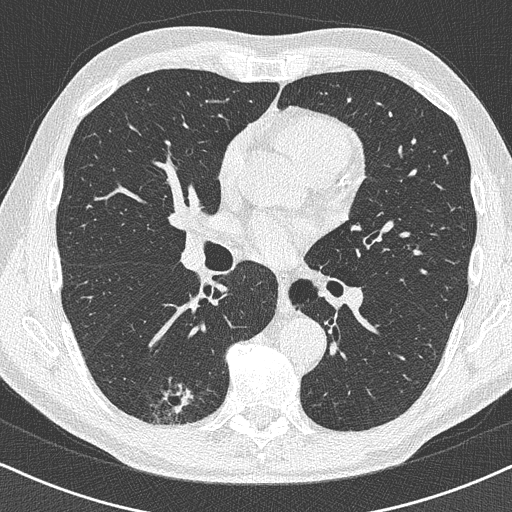
Low-dose screening chest CT, axial slice. Baseline annual screen. Lung window (W 1500 / L -600 HU). Lung (sharp) reconstruction kernel (B50f). Male, age 63 years at enrolment.
Lesion marked by an expert reader, bounding box <138,374,209,431> (left, top, right, bottom; pixels). The exam's reader record, not a measurement of the box and not confirmed to be the same lesion: non-calcified nodule or mass ≥4 mm, right lower lobe, 16 × 13 mm, poorly defined margins. Participant outcome: lung cancer diagnosed 74 days after this screen — adenocarcinoma, NOS, right lower lobe, moderately differentiated (G2), stage IA (AJCC 6th edition), 20 mm at pathology.